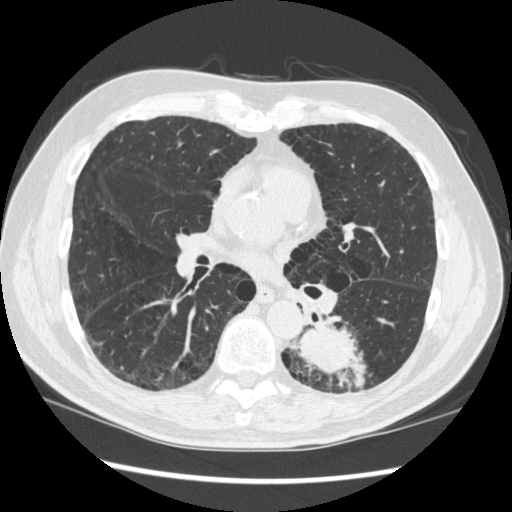
Low-dose screening chest CT, one axial slice; slice 163 of 348 in the series (ordered by position); reconstruction kernel STANDARD; lung window (W 1500 / L -600 HU); 1.25 mm slice thickness; 512 × 512 image matrix.
Structures marked on this image (manually delineated by an expert):
- lesion 1 (tumor, lower lobe of left lung): bounding box <290,325,366,388> (left, top, right, bottom; pixels)